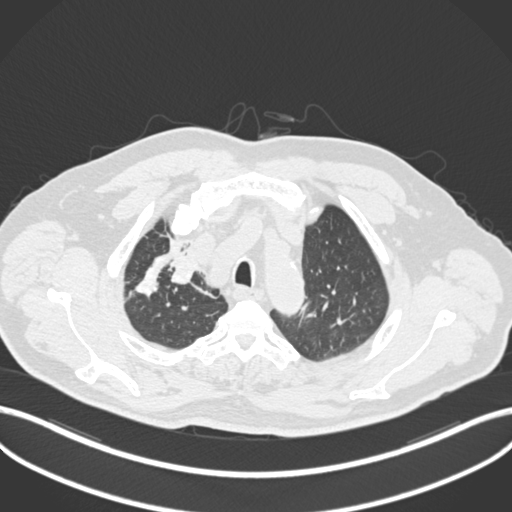
Chest CT, one axial slice. Position 167 of 255 along the scan axis. 120 kVp. Lung window (W 1500 / L -600 HU). 512 × 512 image matrix. Patient: male, 60 years. Case-level facts recorded for this patient, not image findings: clinical TNM (as recorded): T1b N1 M0.
Annotated regions visible in this slice (bounding box drawn by a radiologist):
- lung tumour (recorded histology: squamous cell carcinoma): bounding box <170,249,201,294> (left, top, right, bottom; pixels)